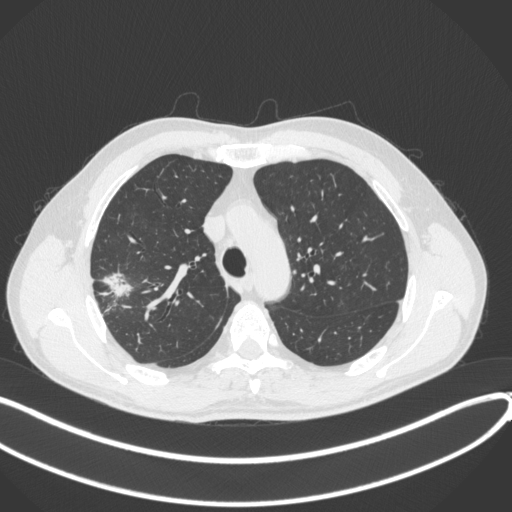
Chest CT, one axial slice; position 308 of 381 along the scan axis; reconstruction kernel B31f; lung window (W 1500 / L -600 HU); 512 × 512 image matrix, field of view 400 × 400 mm. Male patient, age 62 years. From the clinical record (not read from this slice): clinical TNM (as recorded): T1c N0 M0.
Structures marked on this image (rectangle marked by the reading radiologist):
- lung tumour (recorded histology: adenocarcinoma): box from (x=100, y=264) to (x=131, y=298) px